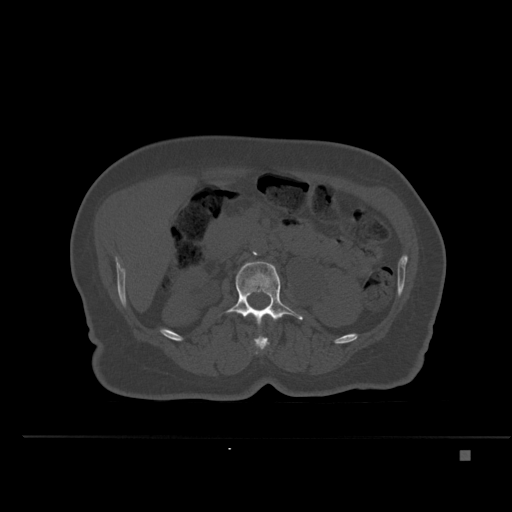
CT including the spine, one axial slice. Position 218 of 477 along the scan axis. Bone window (W 1800 / L 400 HU). 1.5 mm slice thickness. 512 × 512 image matrix, field of view 422 × 422 mm. Female patient, age 74 years. From the clinical record (not read from this slice): primary cancer: colon.
Structures marked on this image (semi-automatic segmentation, software-assisted and operator-edited):
- L1 vertebra: bounding box <251,313,273,354> (left, top, right, bottom; pixels)
- L2 vertebra: <224,261,303,324>